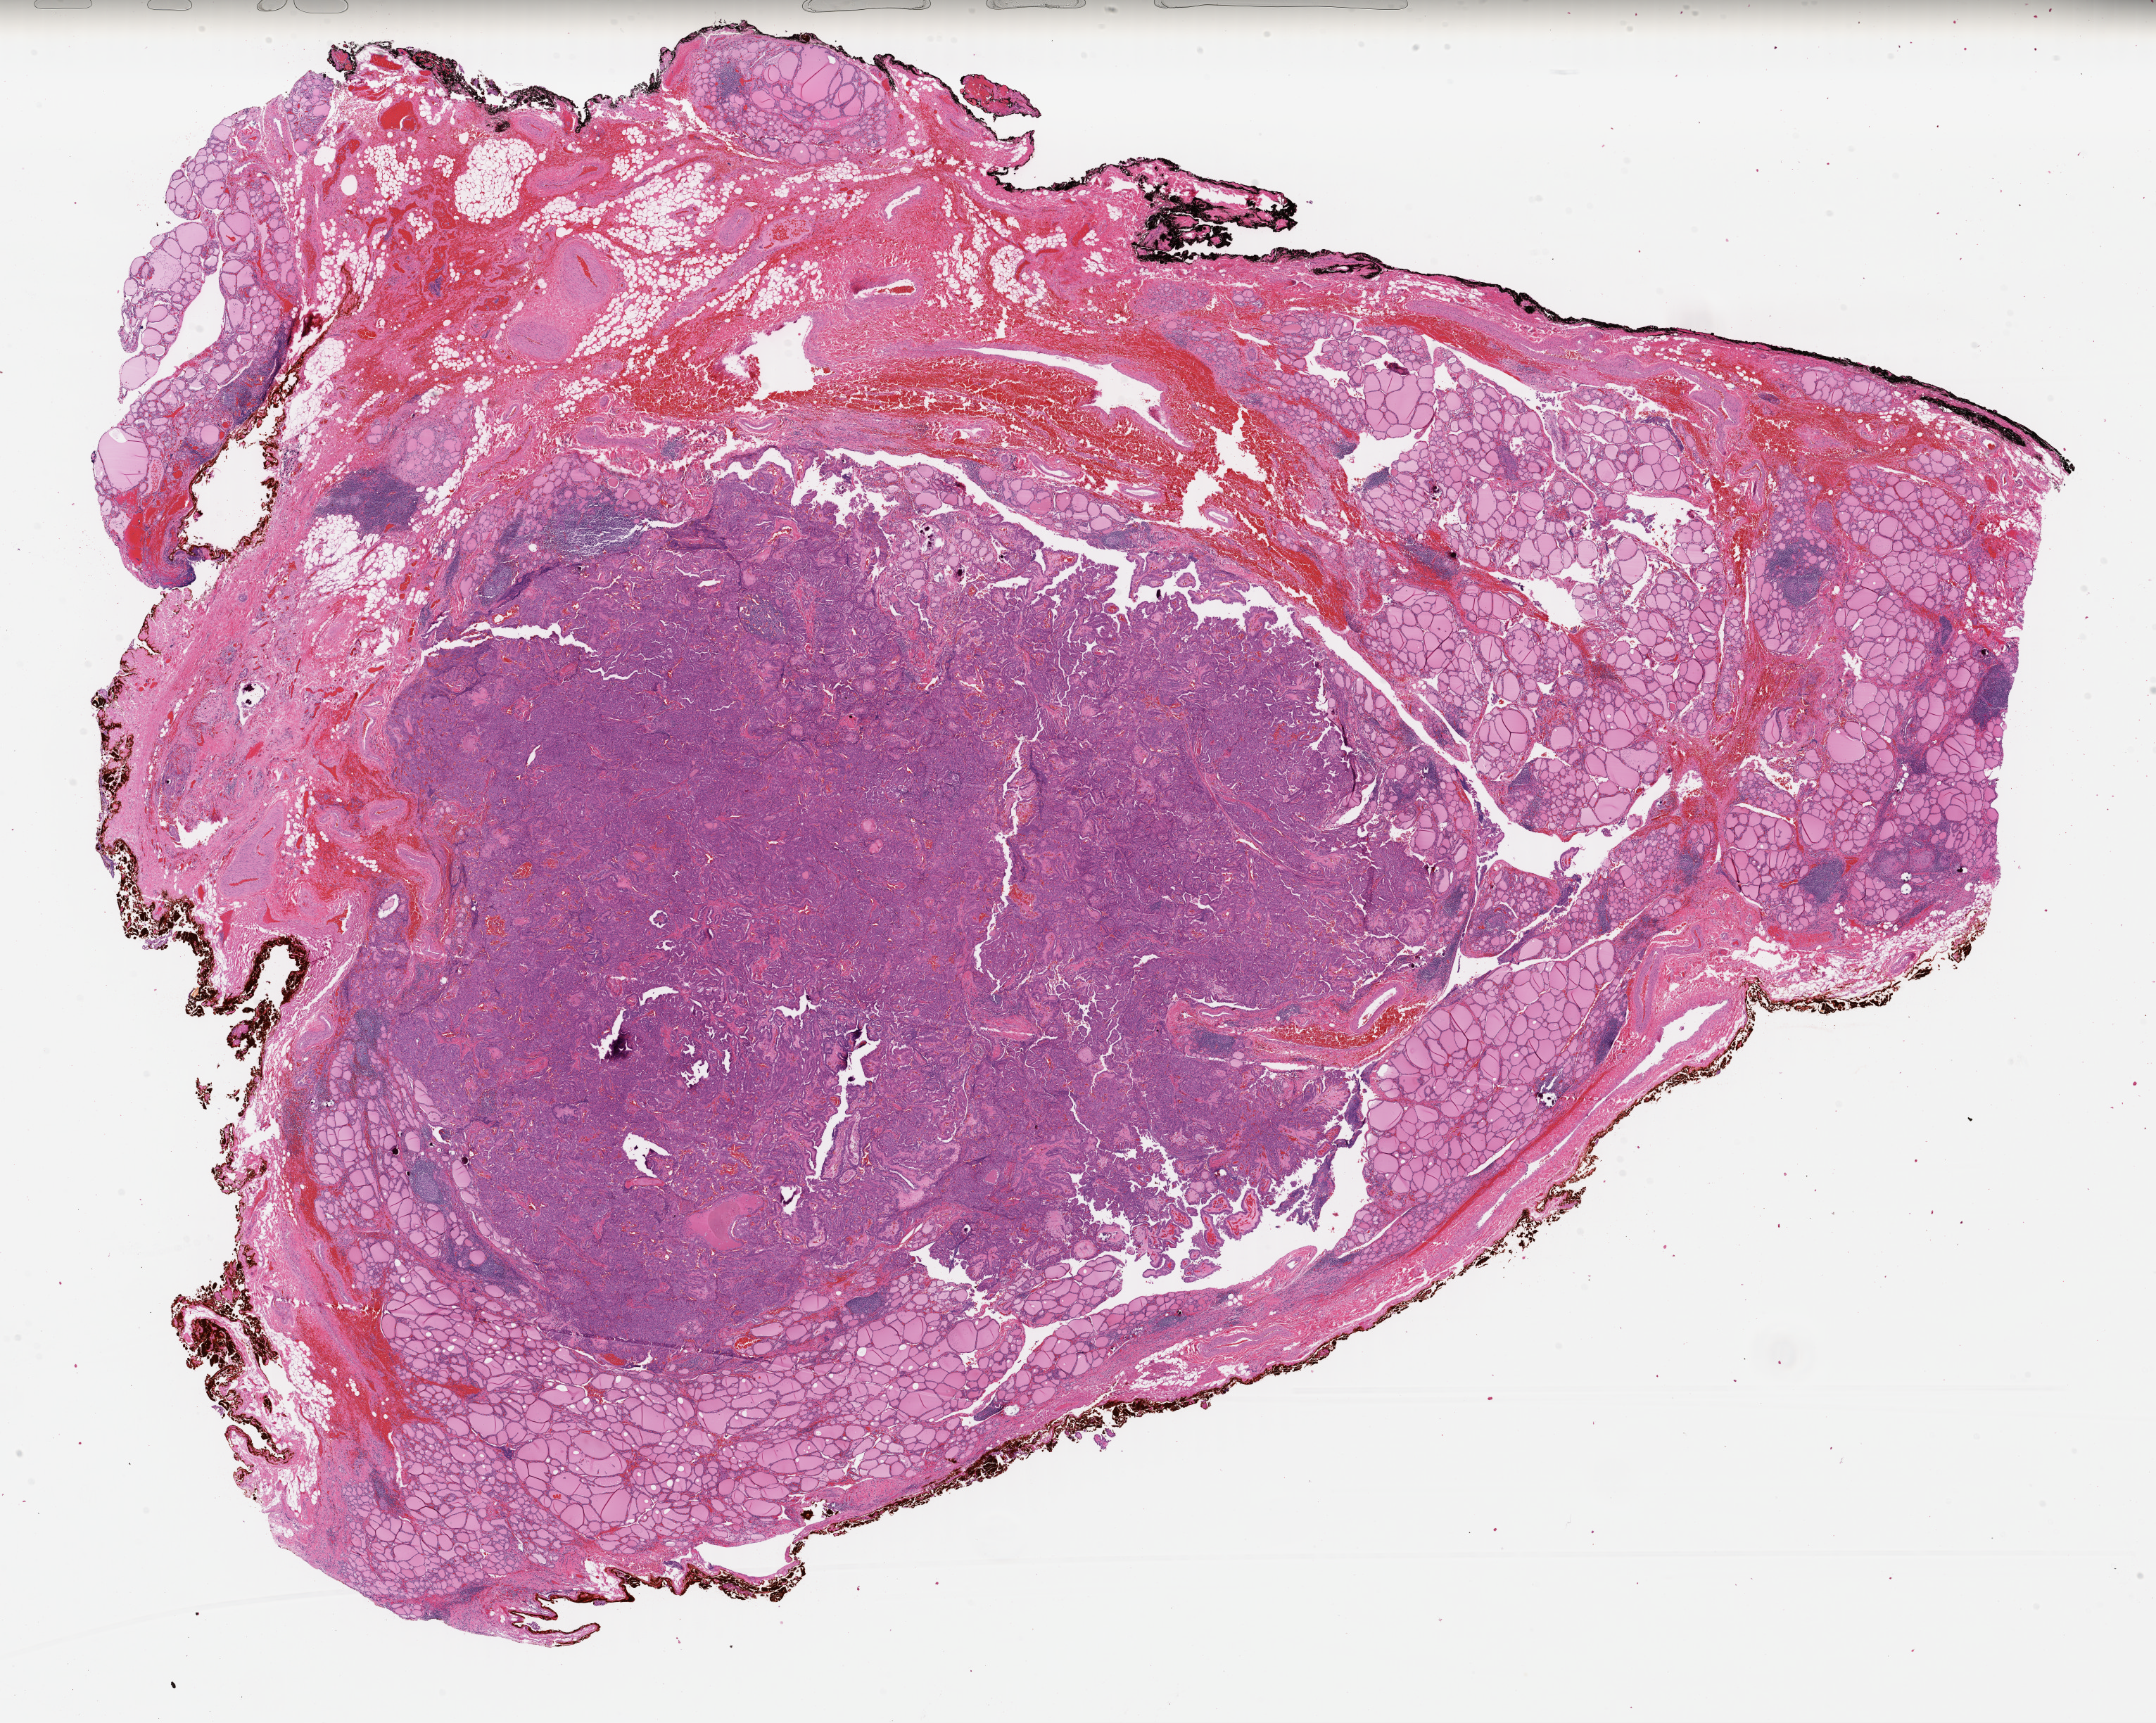
Whole-slide histology image, H&E — a low-resolution overview of the entire scanned area, about 24.1 x 19.2 mm, formalin-fixed paraffin-embedded (FFPE) diagnostic section, sample: primary tumour, thyroid. Female patient; age at initial diagnosis 51 years.
- diagnosis: Papillary adenocarcinoma, NOS (thyroid gland)
- TNM: T1b N1a MX
- AJCC pathologic stage: III (7th edition)
- laterality: right